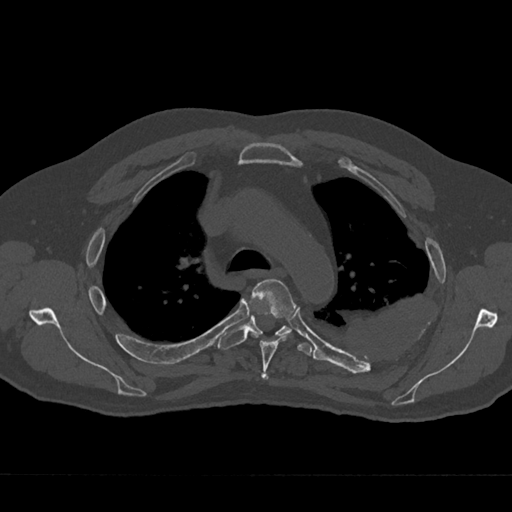
CT including the spine, one axial slice; position 500 of 797 along the scan axis; bone window (W 1800 / L 400 HU); 512 × 512 image matrix, field of view 377 × 377 mm. Patient: male, 75 years. From the clinical record (not read from this slice): primary cancer: renal.
Outlined on this slice (semi-automatically segmented with operator editing):
- T4 vertebra: bounding box [x1, y1, x2, y2] px = [249, 279, 295, 380]
- T5 vertebra: [219, 315, 312, 356]